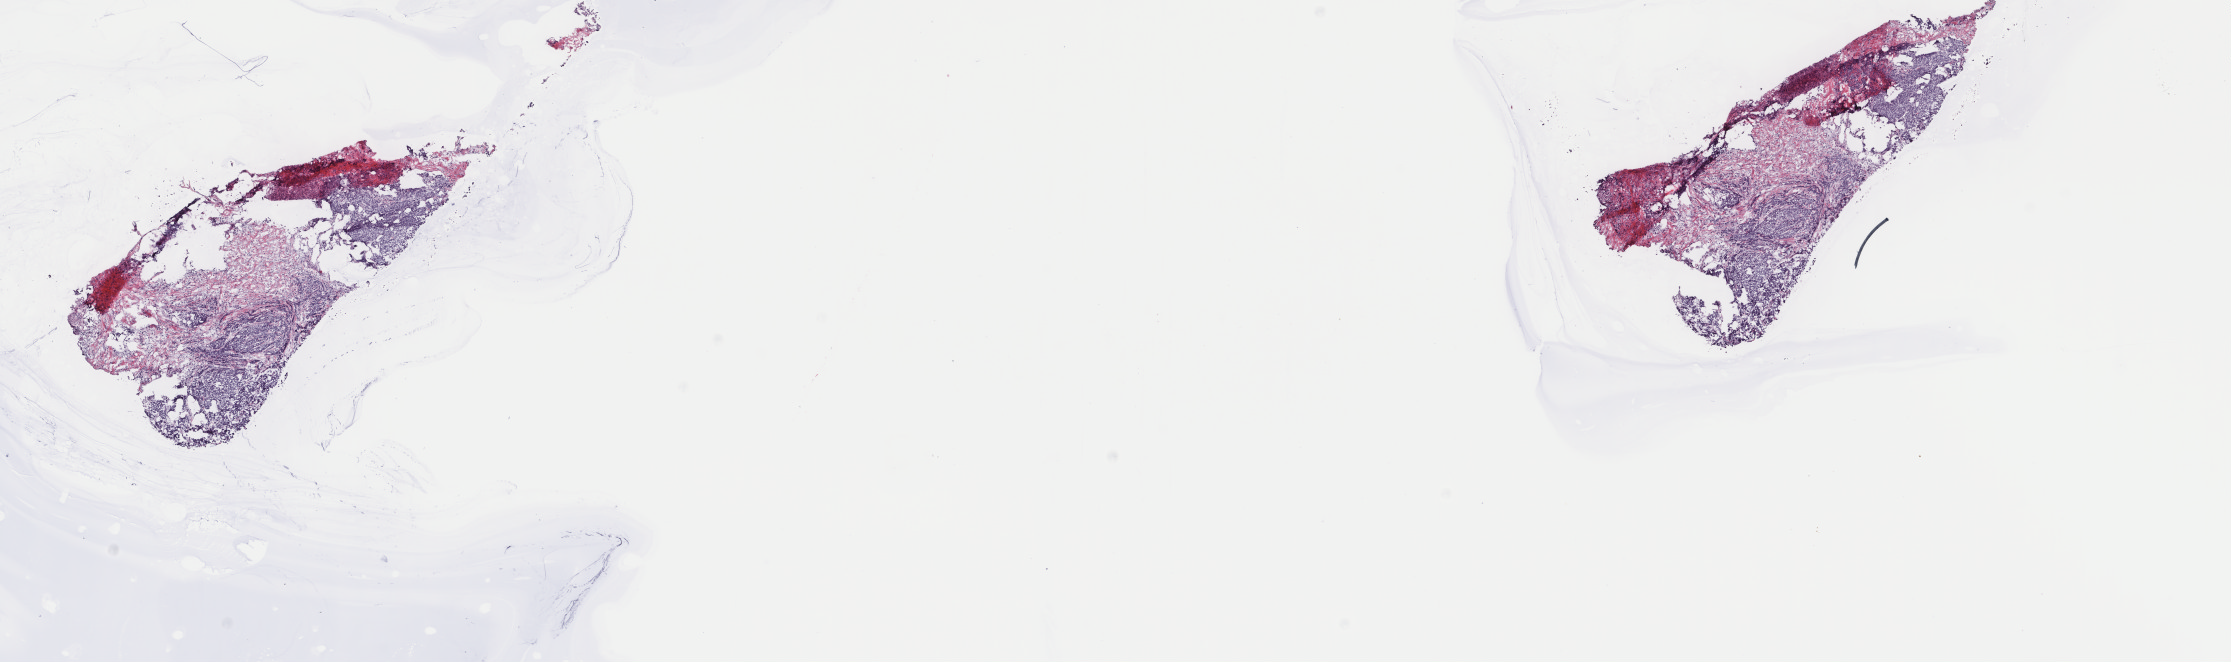
Whole-slide histology image, H&E — low-resolution overview of the scanned area, about 17.7 x 5.3 mm (acquisition: 40x scan), frozen section from the top of the tissue portion, bladder, primary tumour sample. Male patient; age at initial diagnosis 62 years. Histologic grade: high grade. Composition of this section per pathologist review: tumour cells 65%, tumour nuclei 80%, normal cells 0%, stromal cells 35%, necrosis 0%. Infiltration values recorded for this section: lymphocyte infiltration 0%, monocyte infiltration 0%, neutrophil infiltration 0%.
* TNM: T3 N0 M0
* lymph nodes positive (case pathology): 0 of 8 examined
* diagnosis: Transitional cell carcinoma
* AJCC pathologic stage: III (7th edition)